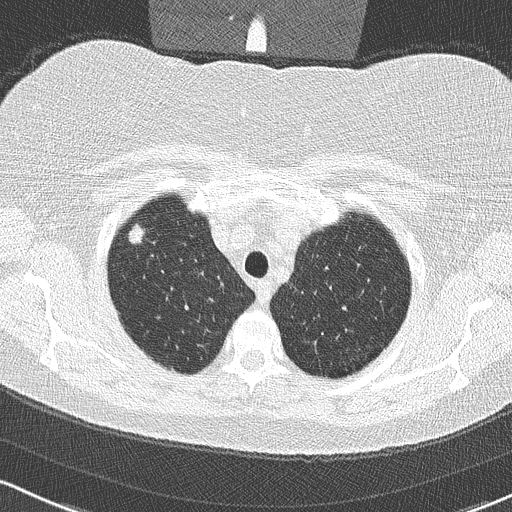
Low-dose screening chest CT, one axial slice. Slice 270 of 315 in the series (ordered by position). Reconstruction kernel B50f. Lung window (W 1500 / L -600 HU). 2 mm slice thickness. 512 × 512 image matrix, field of view 320 × 320 mm.
Outlined on this slice (outlined manually by an expert reader):
- lesion 1 (tumor, upper lobe of right lung): bounding box <128,224,143,244> (left, top, right, bottom; pixels)